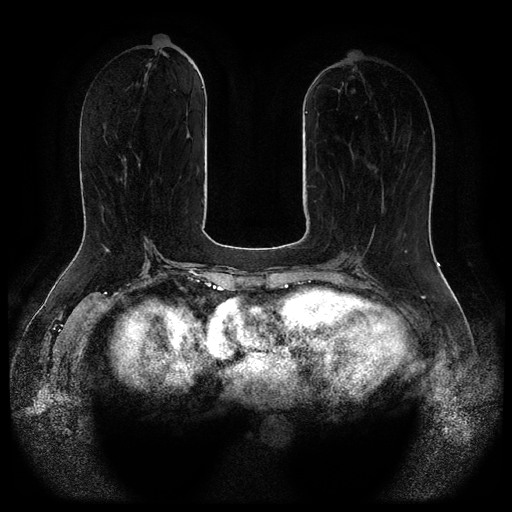
Breast MRI (dynamic contrast-enhanced, multi-phase), one axial slice; dynamic contrast-enhanced series, time point 2 of 5 at this slice position (early post-contrast); 1.5 T; TE 2.6 ms, TR 5.3 ms; 512 × 512 image matrix, field of view 360 × 360 mm. Patient: female, 65 years.
Annotated regions visible in this slice (semi-automatically segmented with operator editing):
- breast lesion (labelled benign in the annotation): bounding box (x1, y1, x2, y2) in pixels: (352, 90, 355, 93)